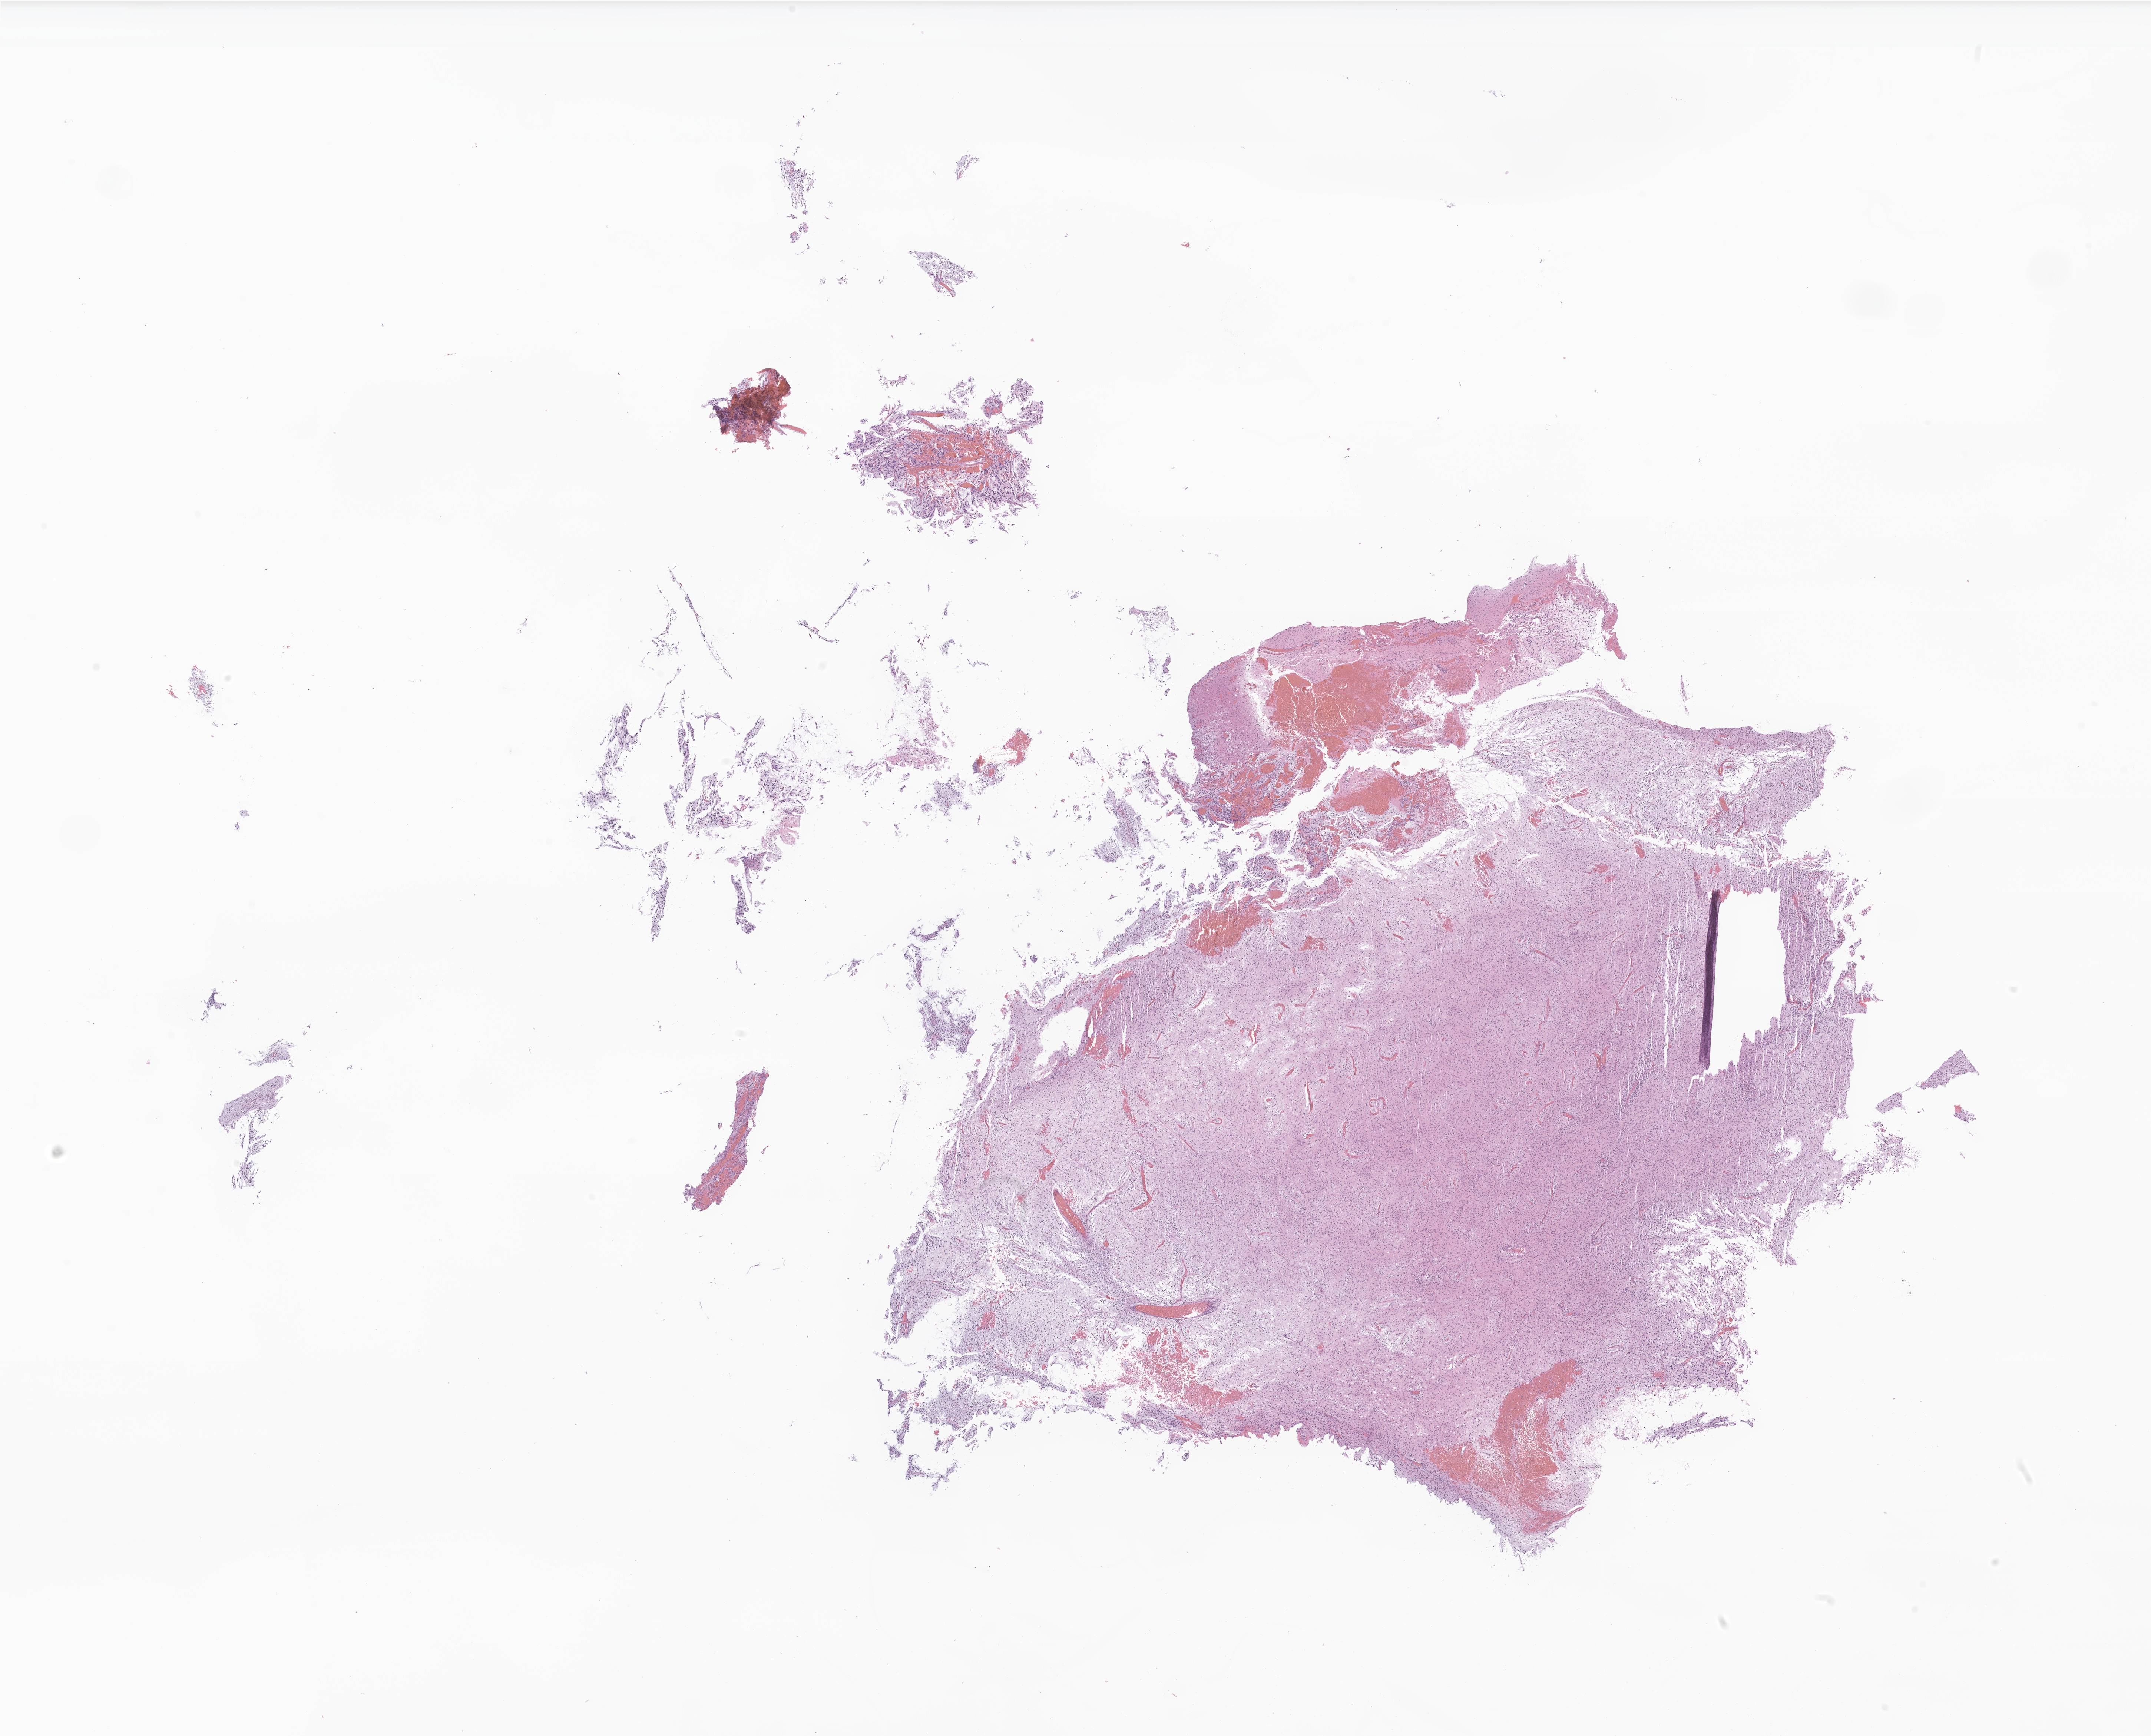
Whole-slide image, H&E stain of tumor tissue from the central nervous system — whole scanned area (about 24.5 x 19.7 mm) shown as a low-resolution overview; FFPE section. Patient female; age 159 months (13 years 3 months).
Diagnosis: Pilocytic astrocytoma.